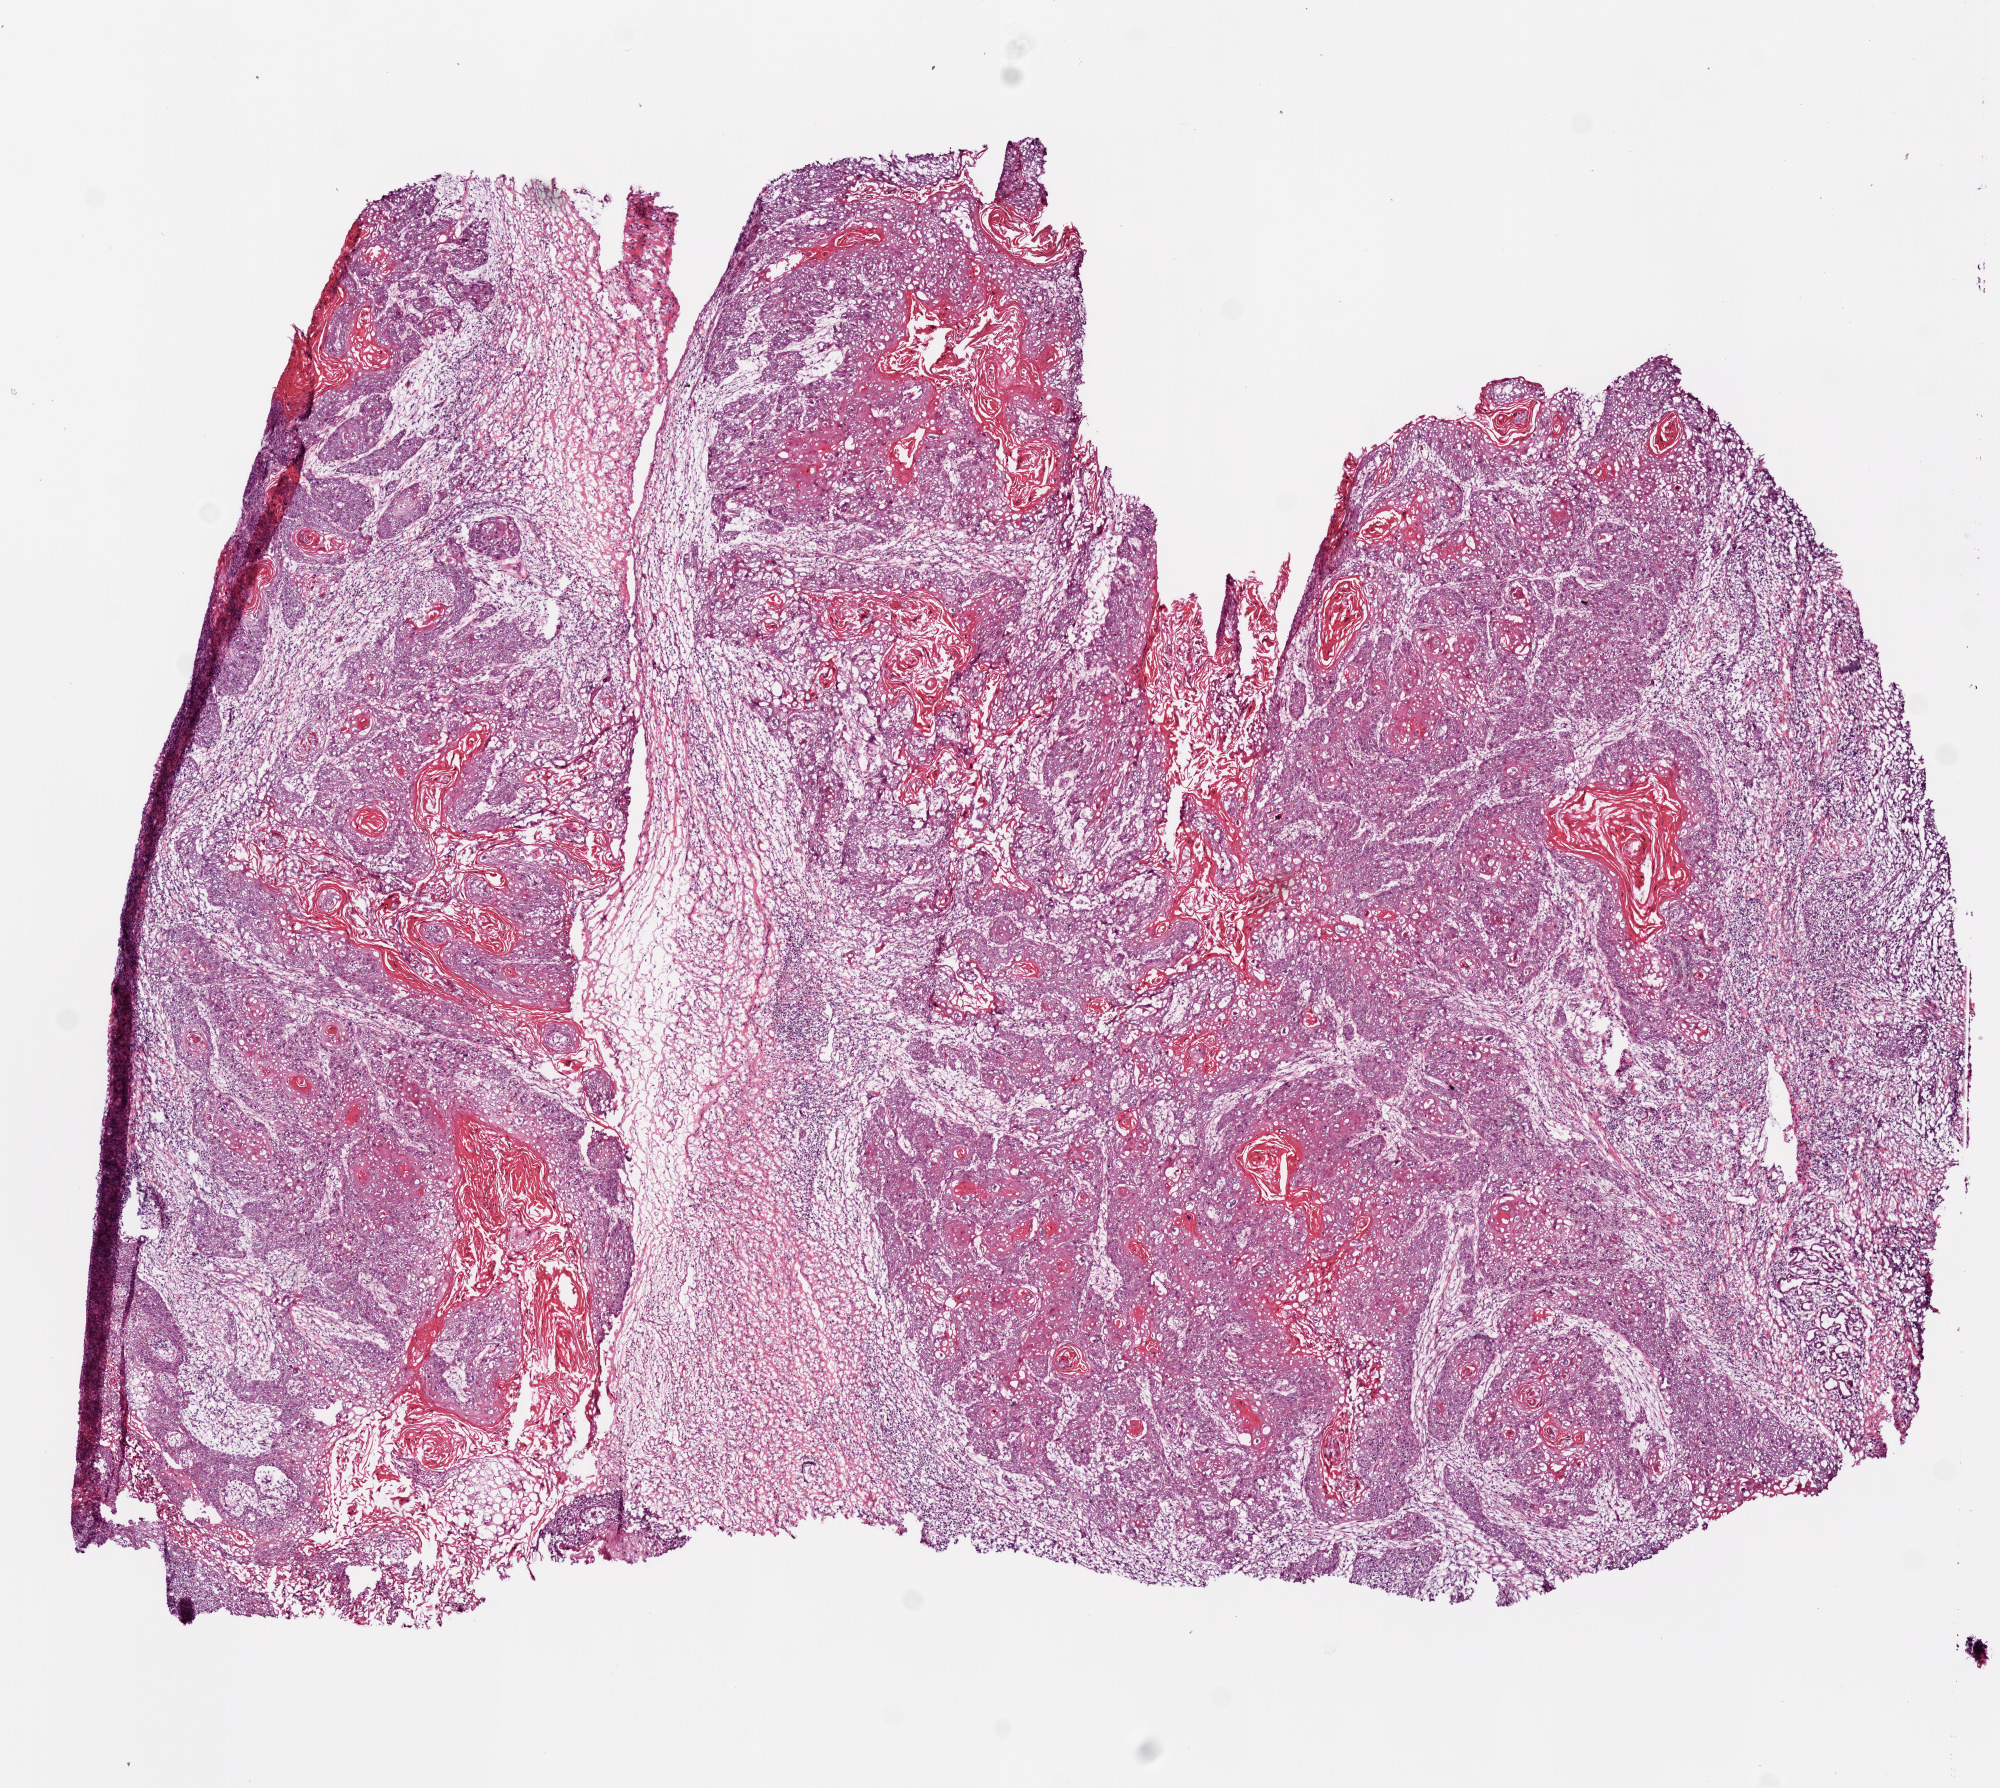
Digitized Hematoxylin and eosin (H&E) stained tissue section (whole slide), shown as a low-resolution overview of the whole scanned area (about 8.0 x 7.2 mm); frozen section from the bottom of the tissue portion; primary tumour sample from the head and neck. Male patient; age at initial diagnosis 64 years. Histologic grade: G2 (moderately differentiated). Pathologist review of this section (percent, as recorded): tumour cells 80%, tumour nuclei 80%, normal cells 0%, stromal cells 20%, necrosis 0%.
- TNM: T4a N0
- AJCC pathologic stage: IVA
- pathologic diagnosis: Squamous cell carcinoma, NOS (larynx, NOS)